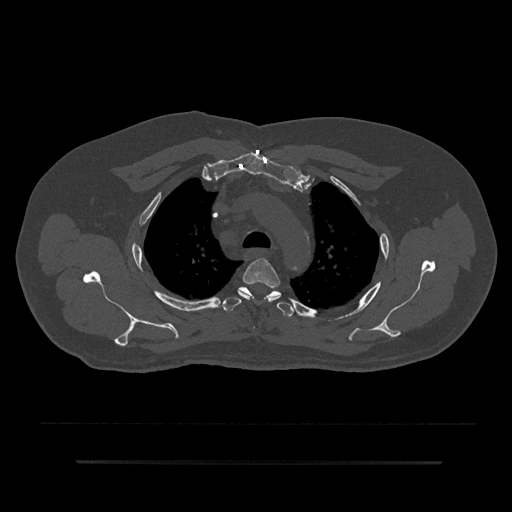
CT including the spine, one axial slice; position 642 of 797 along the scan axis; bone window (W 1800 / L 400 HU); 0.5 mm slice thickness; 512 × 512 image matrix, field of view 464 × 464 mm. Patient: male, 59 years. Case-level facts recorded for this patient, not image findings: primary cancer: bile ducts.
Annotated regions visible in this slice (semi-automatically segmented with operator editing):
- T3 vertebra: bounding box <238,258,281,299> (left, top, right, bottom; pixels)
- T4 vertebra: <222,286,294,317>